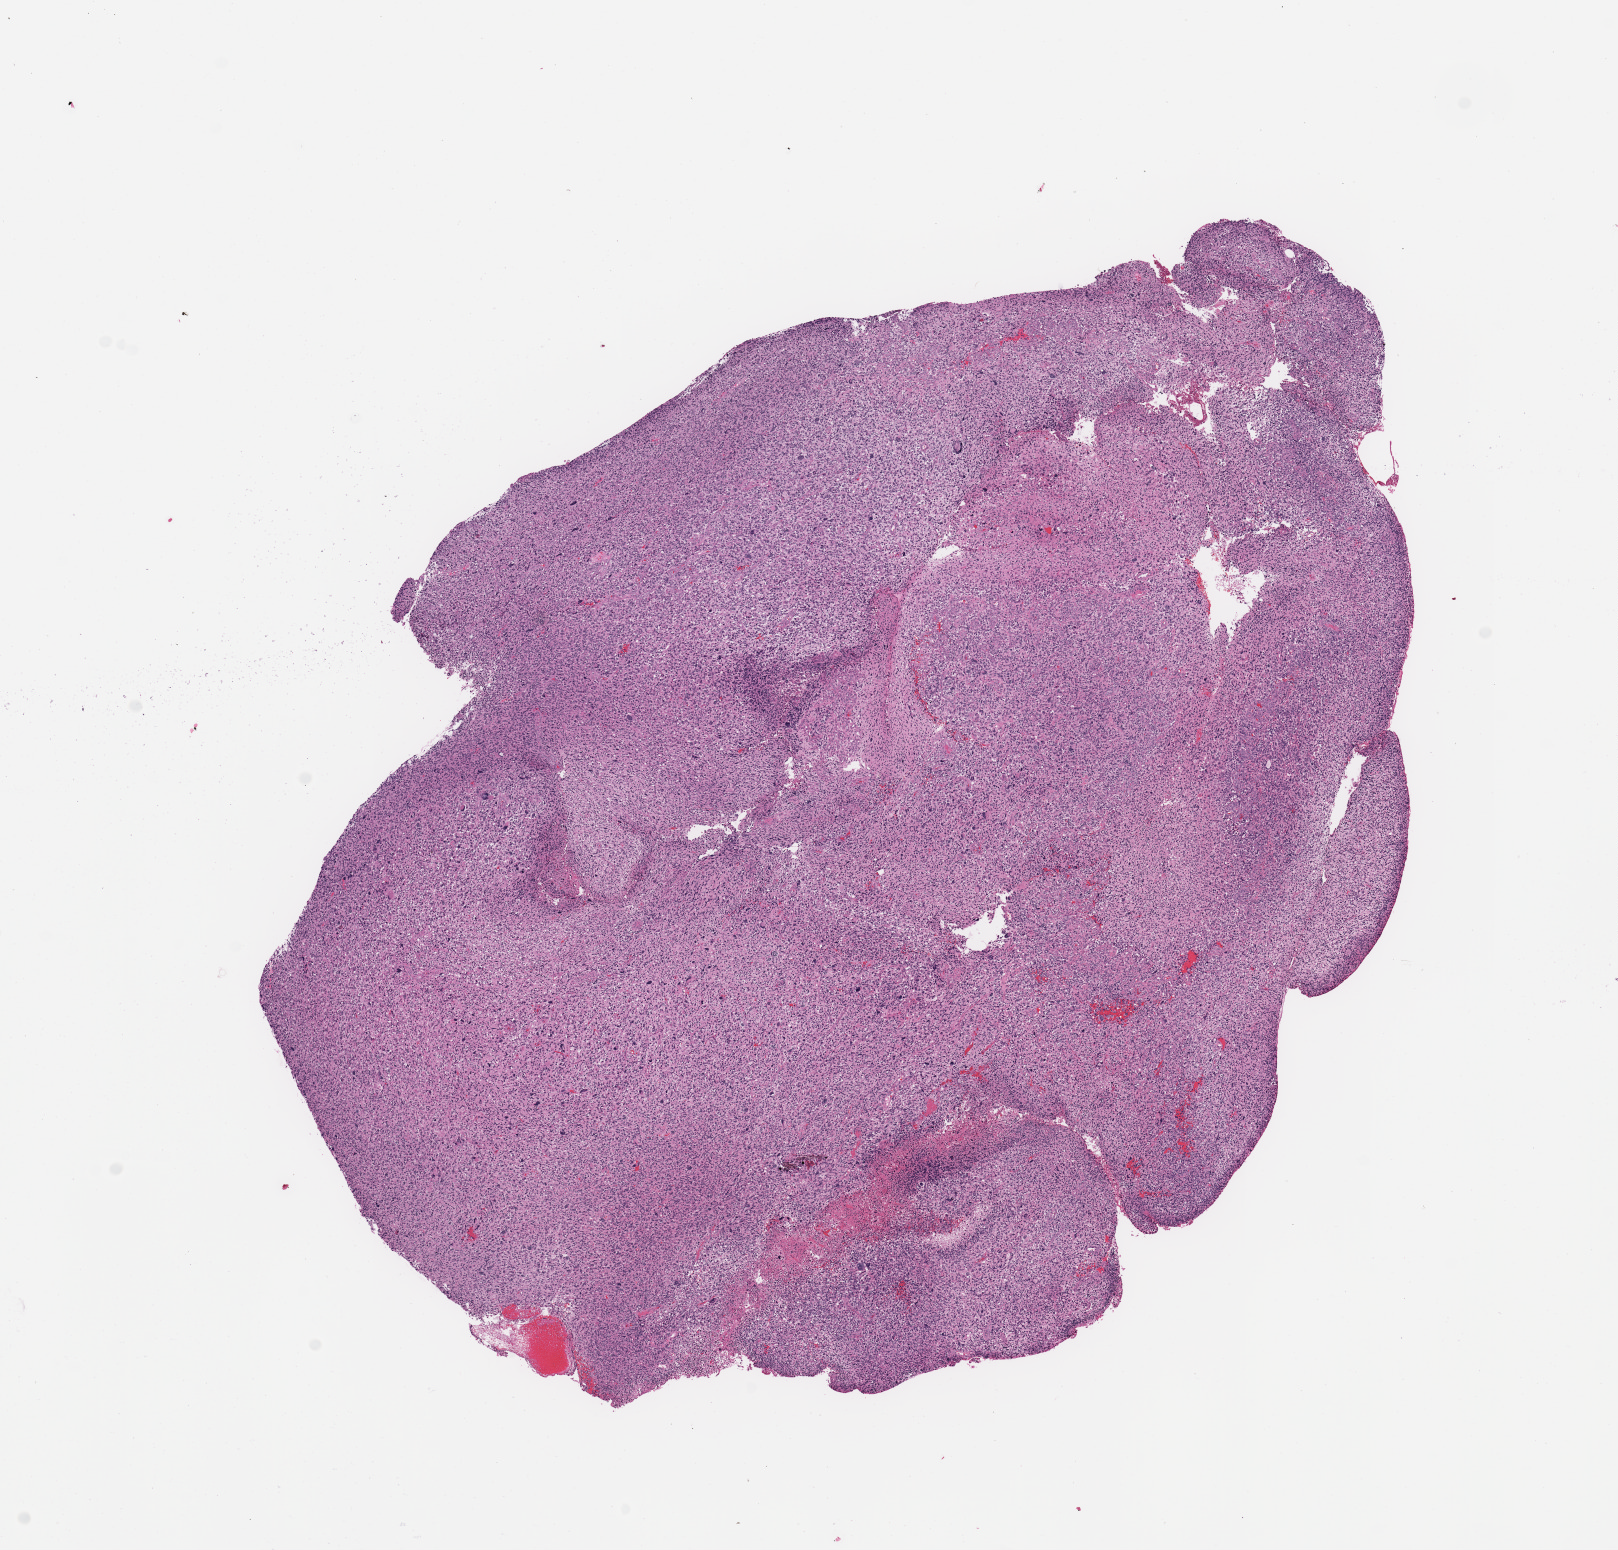
Whole-slide histology image, Hematoxylin and eosin (H&E) stained — low-resolution overview of the scanned area, about 12.8 x 12.3 mm, brain, tumour tissue. 60-year-old male patient.
Diagnosis: Glioblastoma.